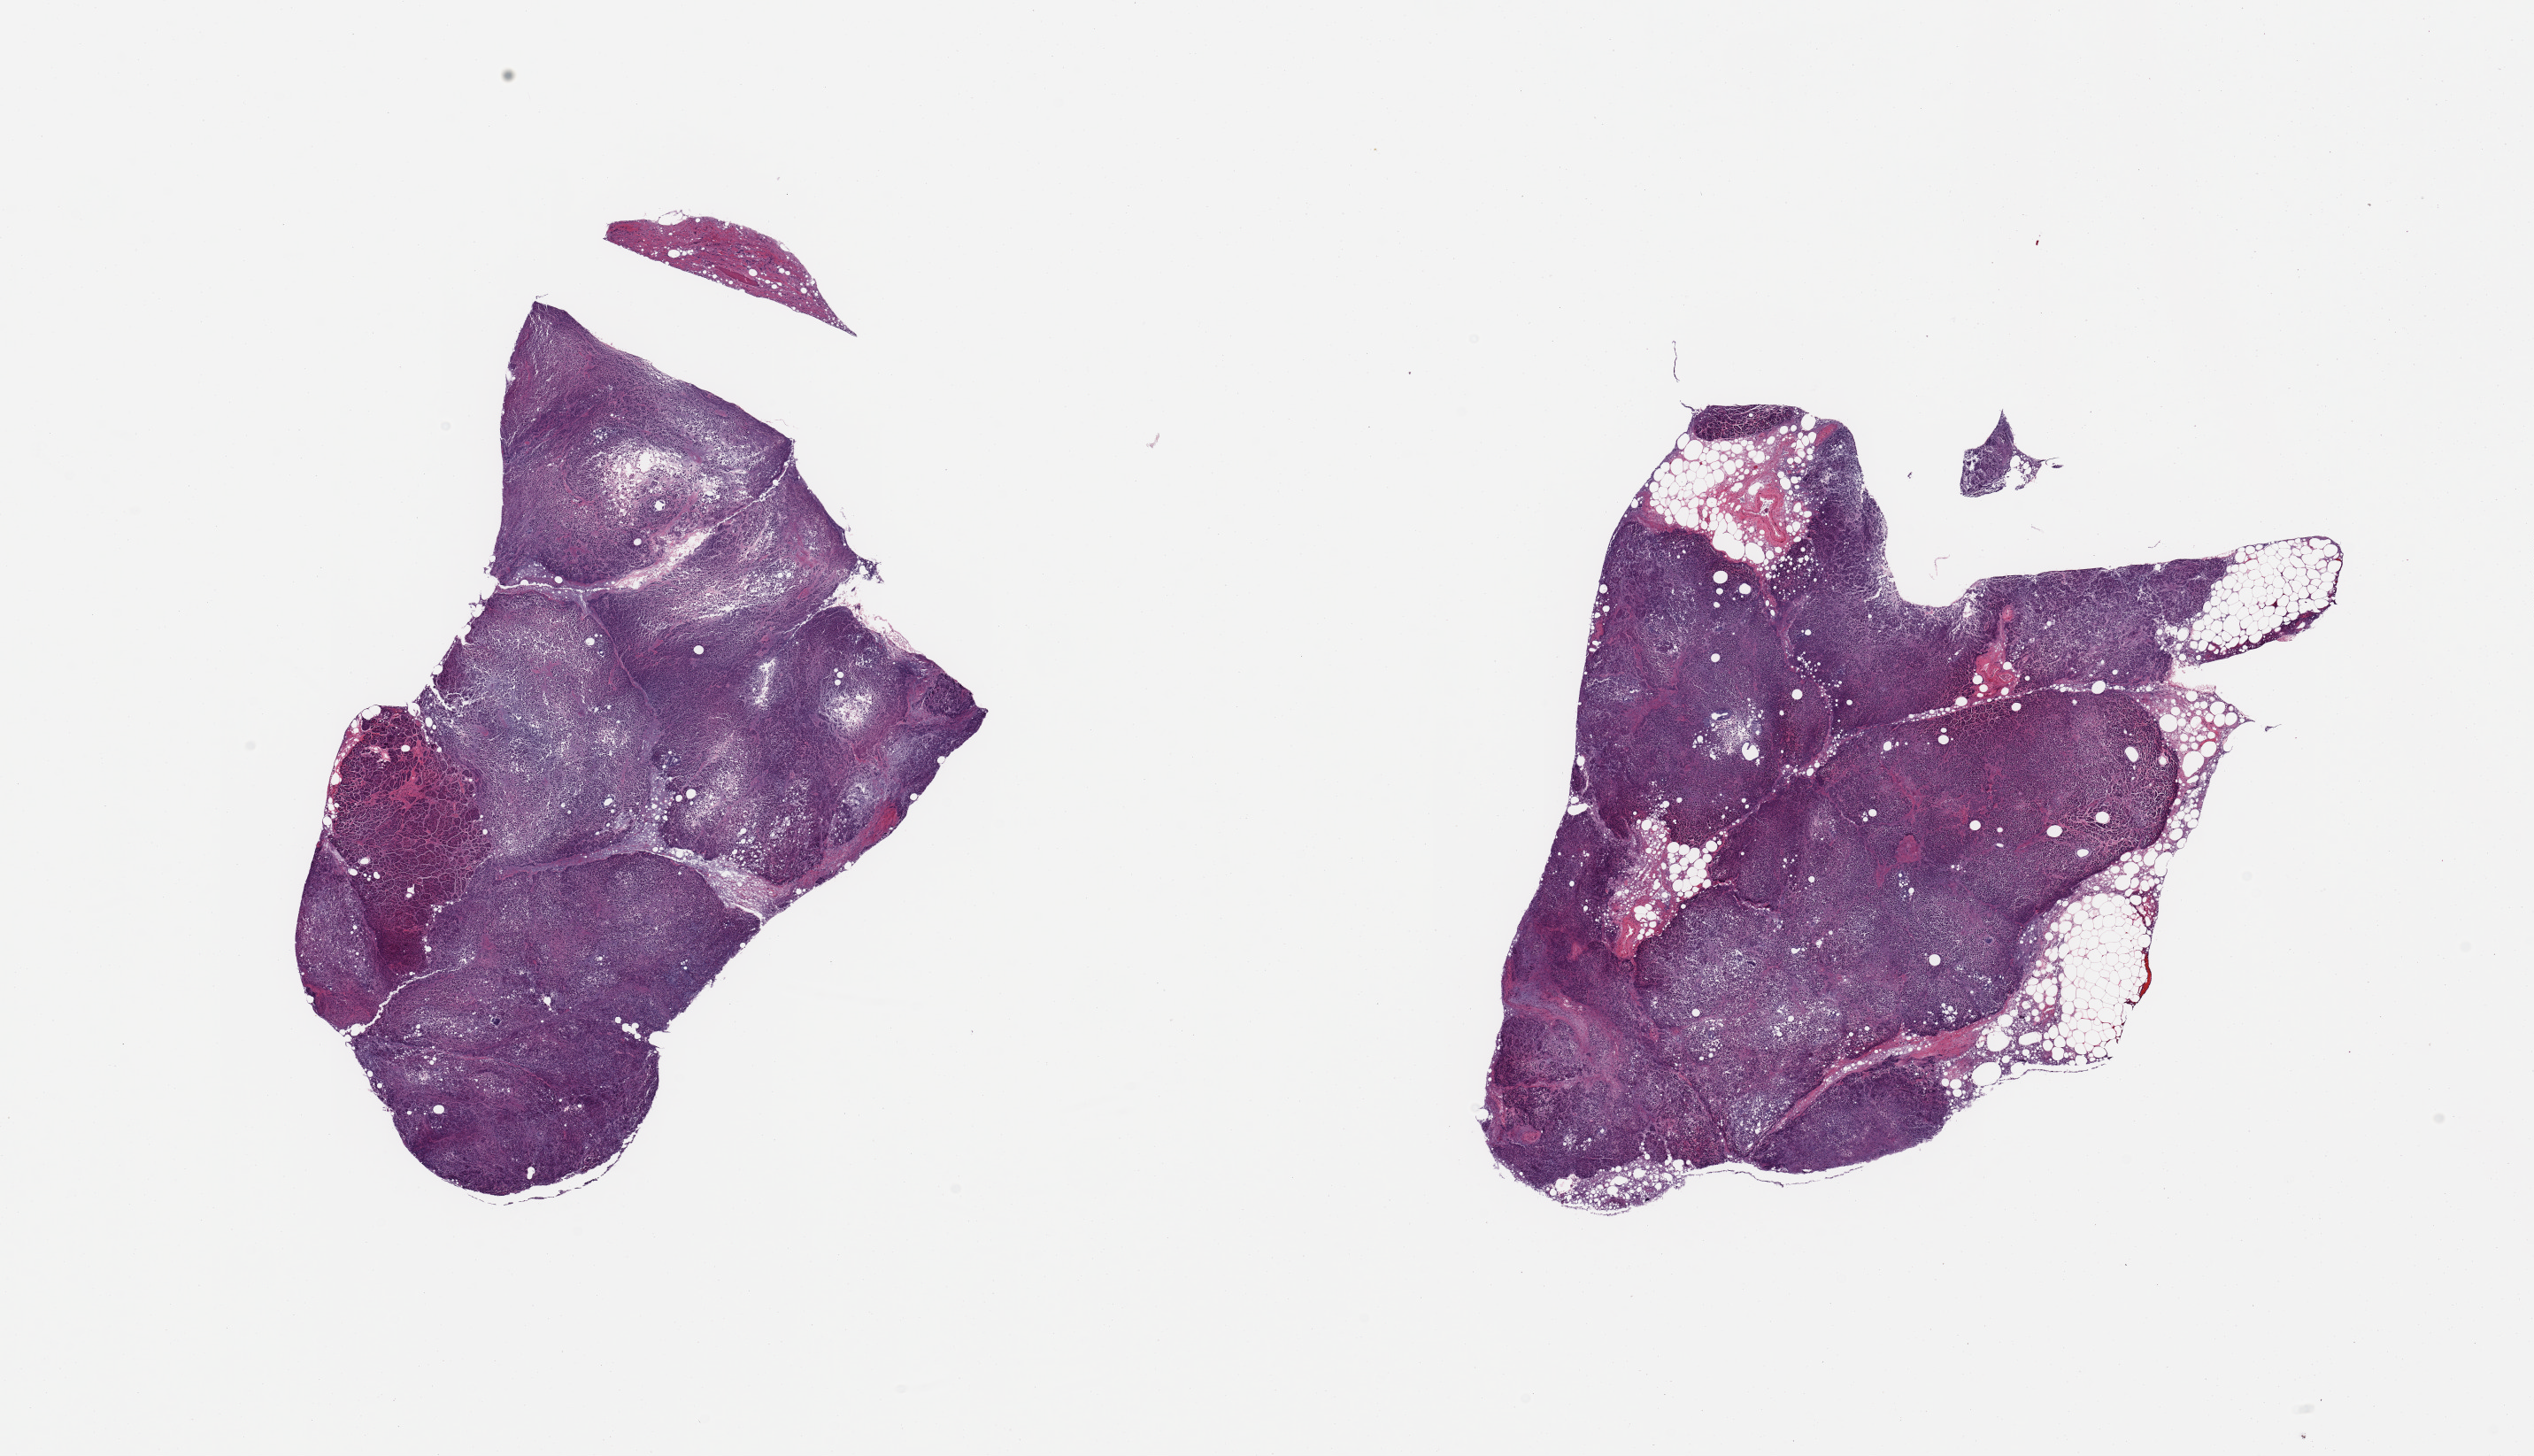
H&E whole-slide image, brightfield, whole scanned area (about 22.6 x 13.0 mm) shown as a low-resolution overview; PAXgene-fixed, paraffin-embedded tissue; target tissue: pancreas; donor tissue sample. Donor: male.
• reviewer comment on this tissue sample: 2 pieces; totally autolyzed